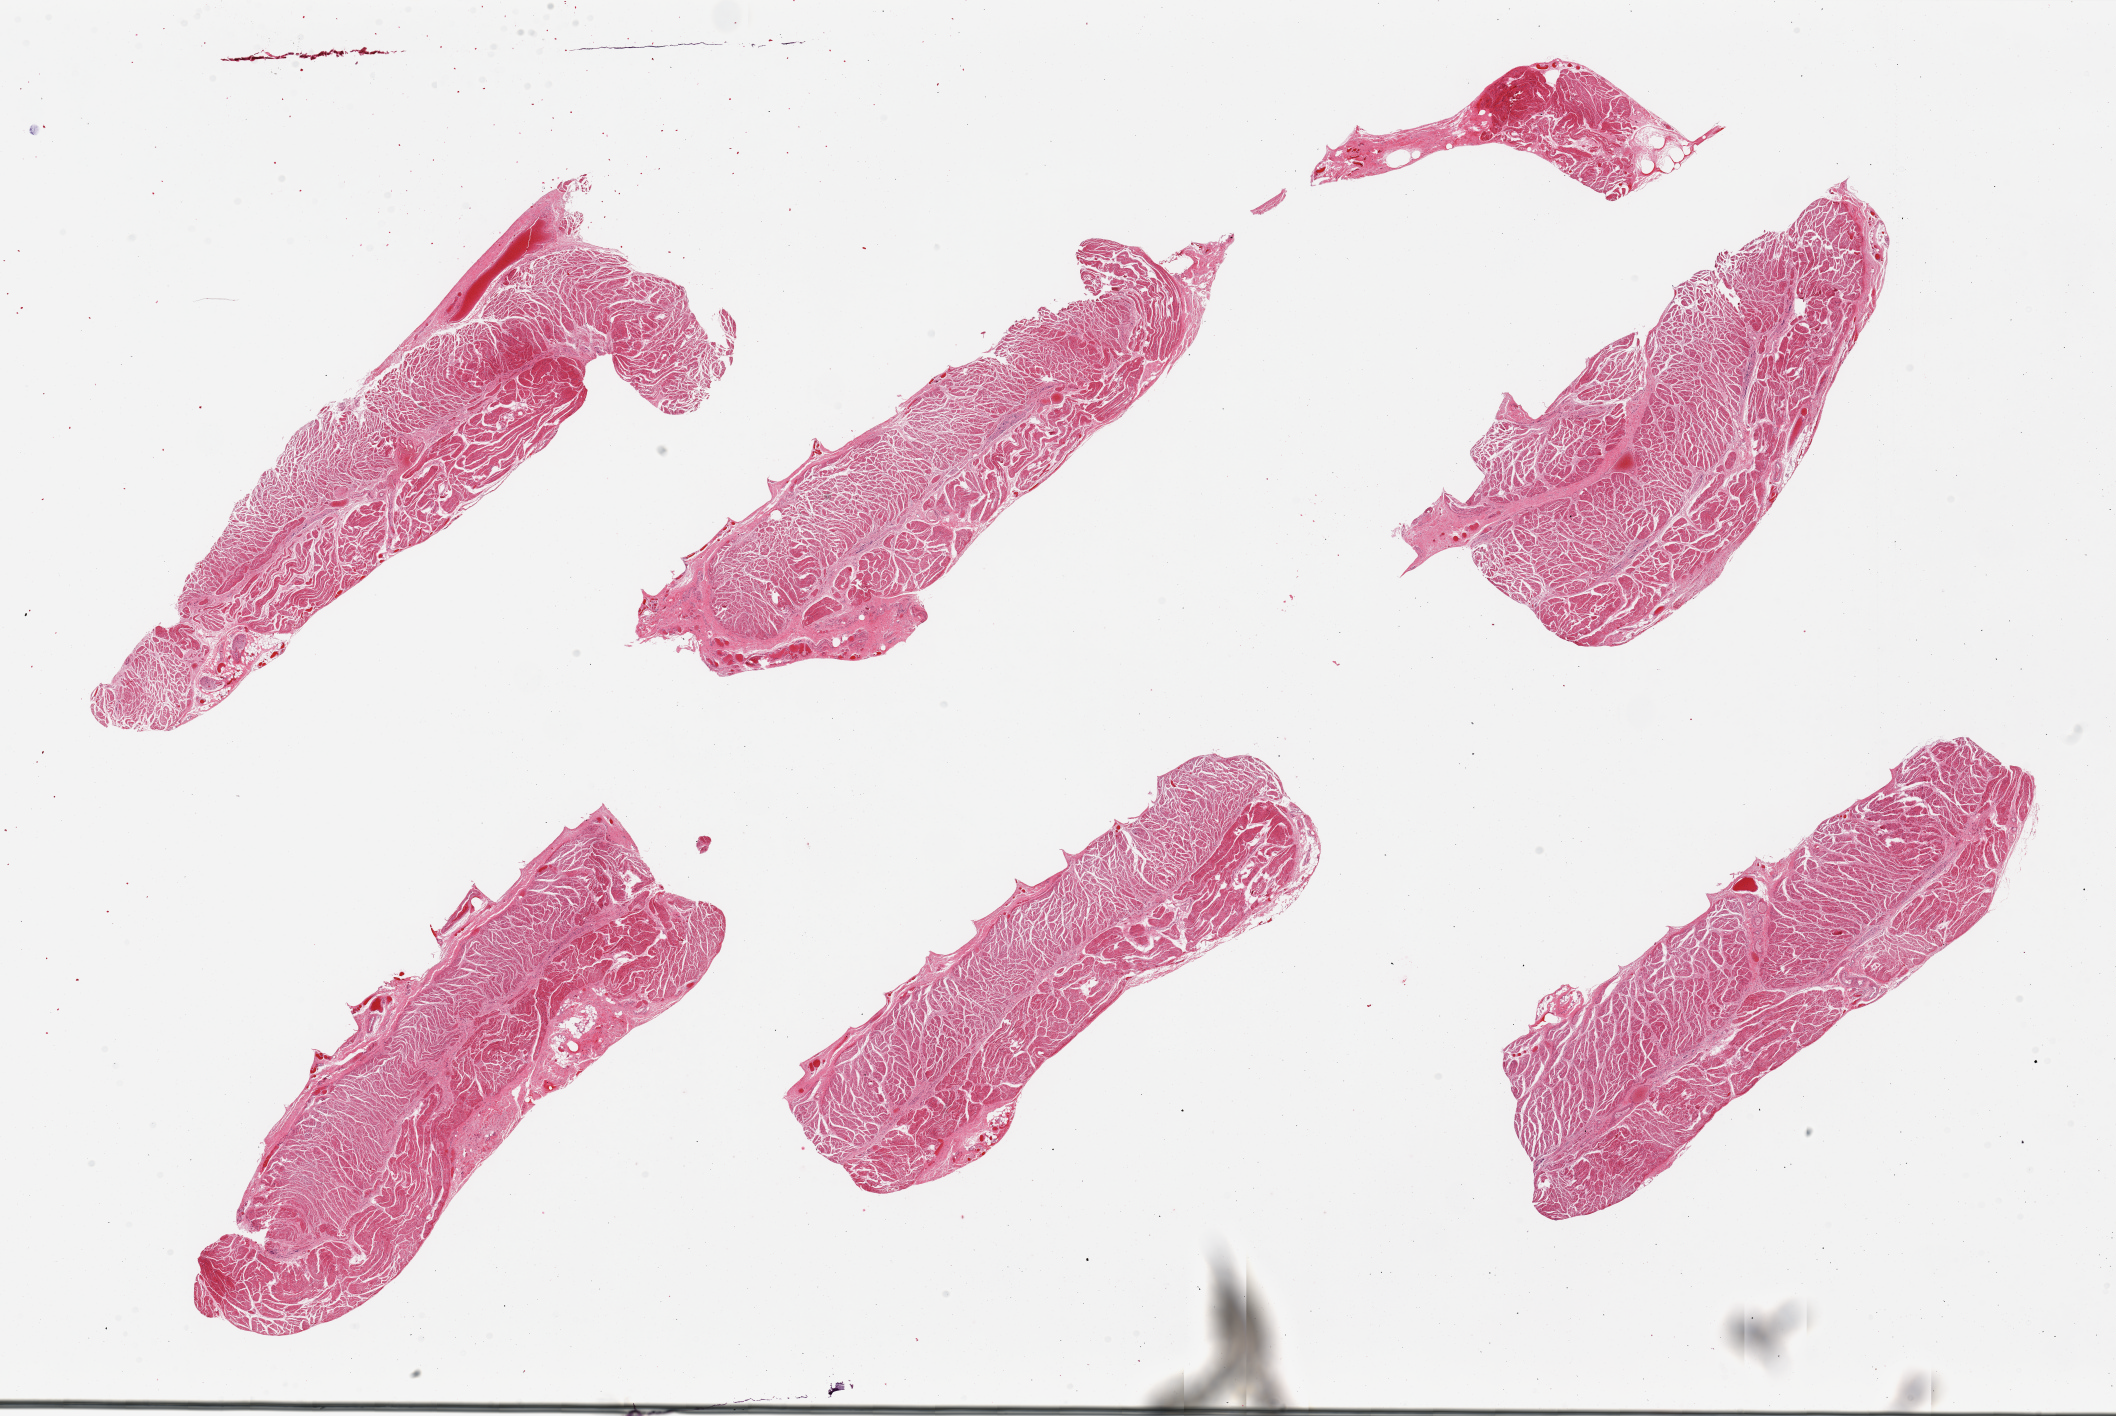
Whole-slide image, hematoxylin and eosin (H&E) stain, brightfield, shown as a low-resolution overview of the whole scanned area (about 33.5 x 22.4 mm), PAXgene-fixed paraffin-embedded (PFPE) section, section of gastroesophageal junction (target tissue), tissue donor sample. Donor: male.
Review note (as recorded): 6 pieces, all muscularis.